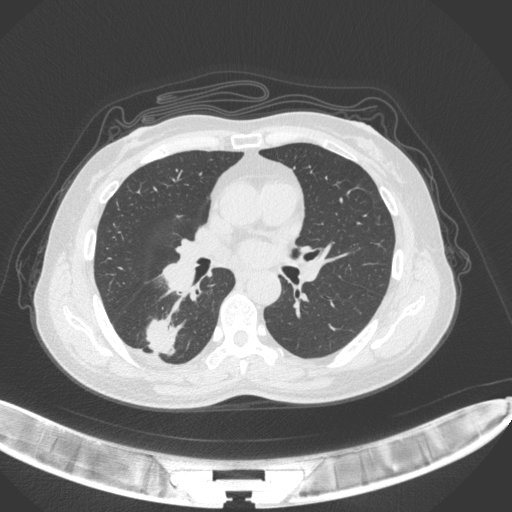
Chest CT, one axial slice. Reconstruction kernel B31f. 120 kVp. Lung window (W 1500 / L -600 HU). 1 mm slice thickness. 512 × 512 image matrix, field of view 400 × 400 mm. Patient: female, 55 years. Case-level facts recorded for this patient, not image findings: clinical TNM (as recorded): T1c N1 M0.
Outlined on this slice (bounding box drawn by a radiologist):
- lung tumour (recorded histology: adenocarcinoma): bounding box <145,318,187,356> (left, top, right, bottom; pixels)